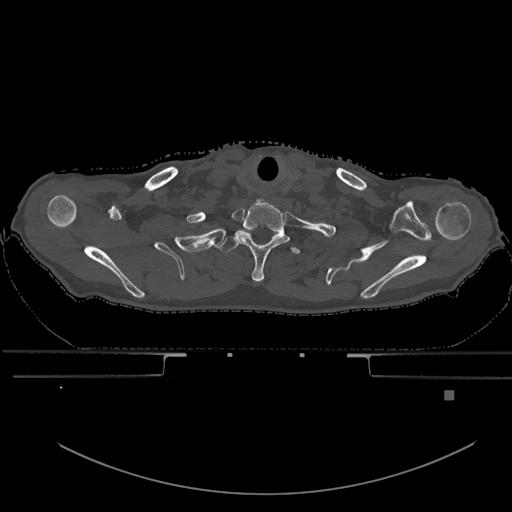
CT including the spine, one axial slice; position 565 of 969 along the scan axis; bone window (W 1800 / L 400 HU); 512 × 512 image matrix, field of view 456 × 456 mm. Male patient, age 82 years. From the clinical record (not read from this slice): primary cancer: prostate; vertebrae with lytic lesions (as recorded): T11, T9, T8, T2.
Structures marked on this image (semi-automatically segmented with operator editing):
- T1 vertebra: bounding box [x1, y1, x2, y2] px = [218, 237, 300, 255]